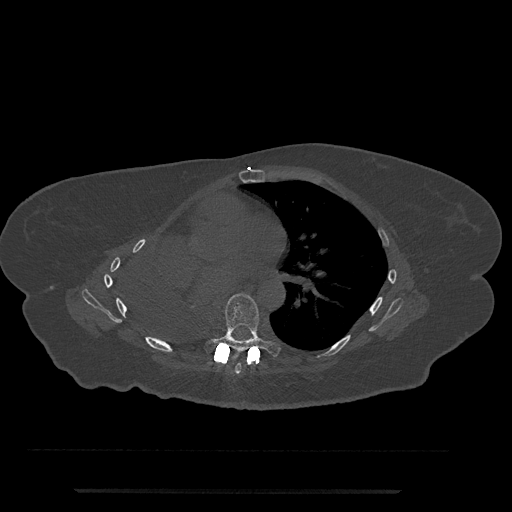
CT including the spine, one axial slice. Slice 448 of 797 in the series (ordered by position). Reconstruction kernel Br40s/3. 120 kVp. Bone window (W 1800 / L 400 HU). 512 × 512 image matrix, field of view 440 × 440 mm. Female patient, age 51 years. Case-level facts recorded for this patient, not image findings: primary cancer: neuro; vertebrae with lytic lesions (as recorded): T8.
Structures marked on this image (semi-automatically segmented with operator editing):
- T6 vertebra: bounding box [x1, y1, x2, y2] px = [235, 363, 242, 374]
- T7 vertebra: [205, 293, 281, 356]